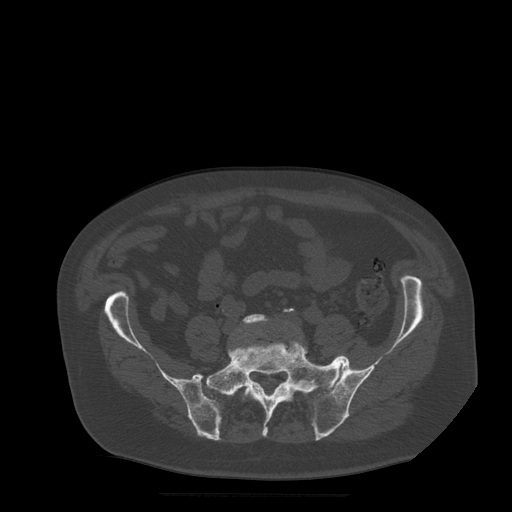
CT including the spine, one axial slice. Slice 70 of 522 in the series (ordered by position). Bone window (W 1800 / L 400 HU). 1.25 mm slice thickness. 512 × 512 image matrix, field of view 420 × 420 mm. Patient age 72 years. Case-level facts recorded for this patient, not image findings: primary cancer: prostate.
Annotated regions visible in this slice (semi-automatically segmented with operator editing):
- L5 vertebra: bounding box [x1, y1, x2, y2] px = [243, 314, 293, 397]